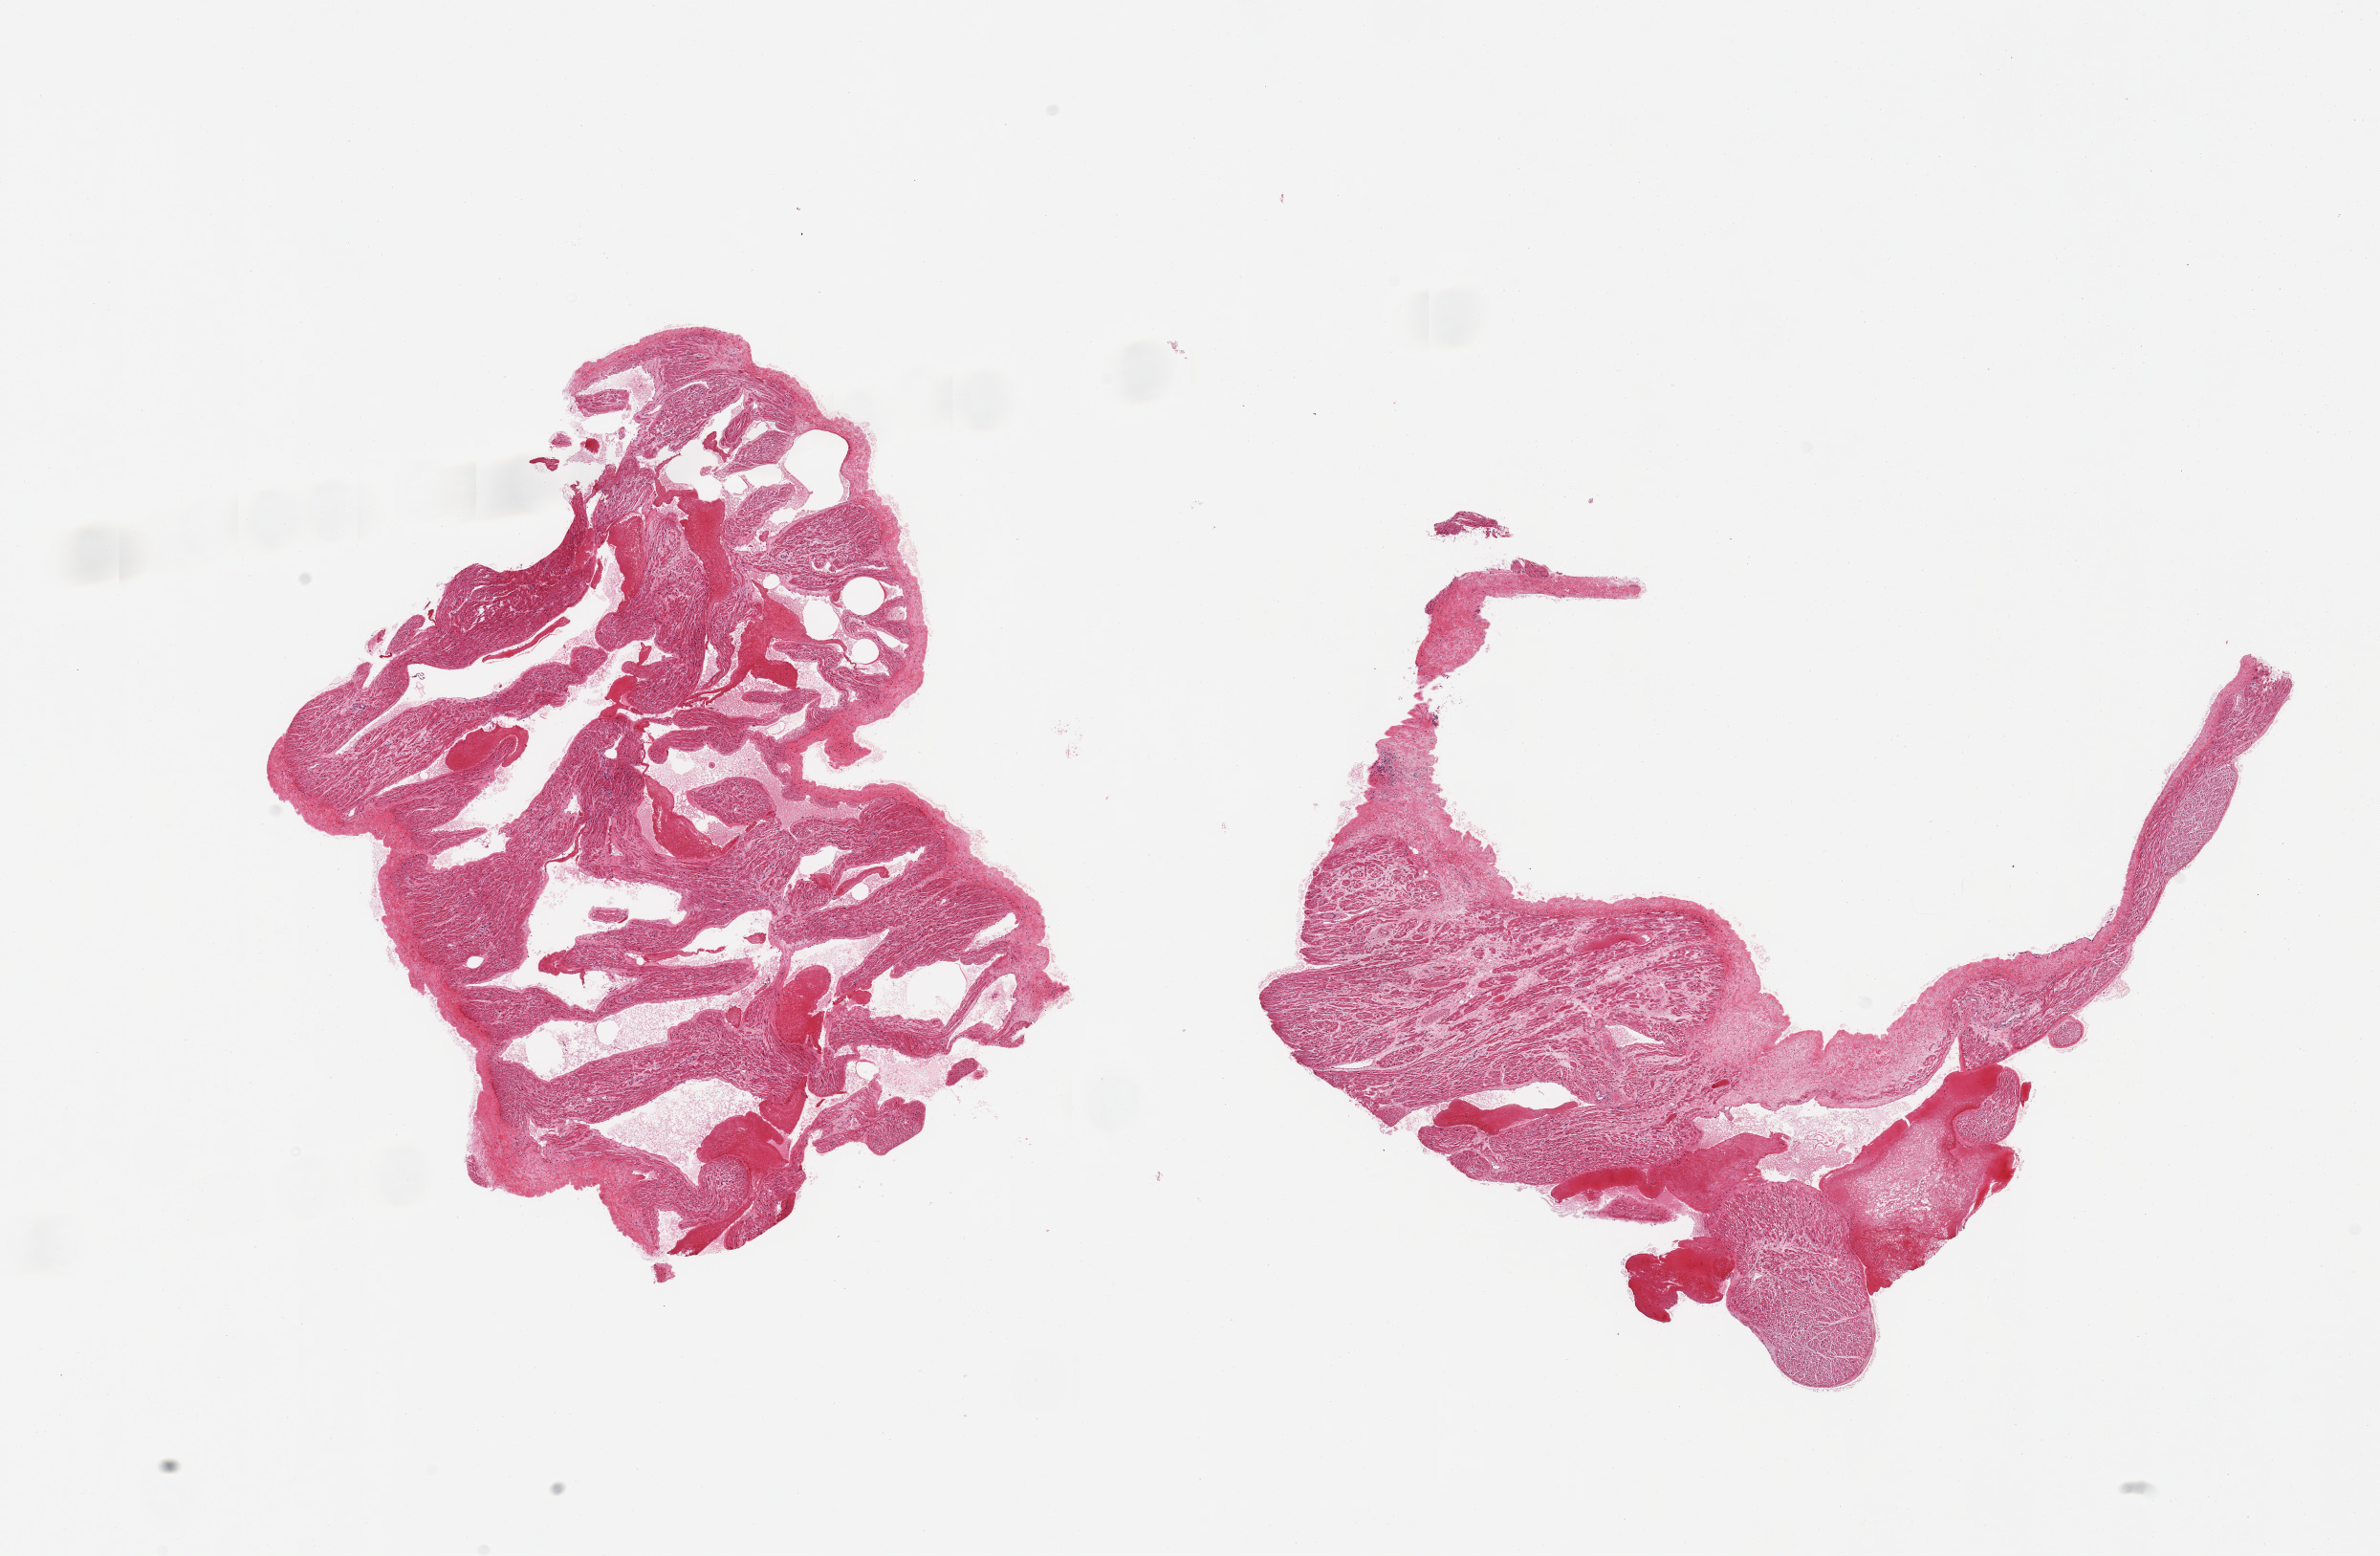
Whole-slide image, H&E stain, brightfield, low-resolution overview of the scanned area, about 19.7 x 12.9 mm, PAXgene-fixed, paraffin-embedded tissue, target tissue: auricular appendage, donor tissue sample.
Pathologist's review note for this sample: 2 pieces, no abnormalities.